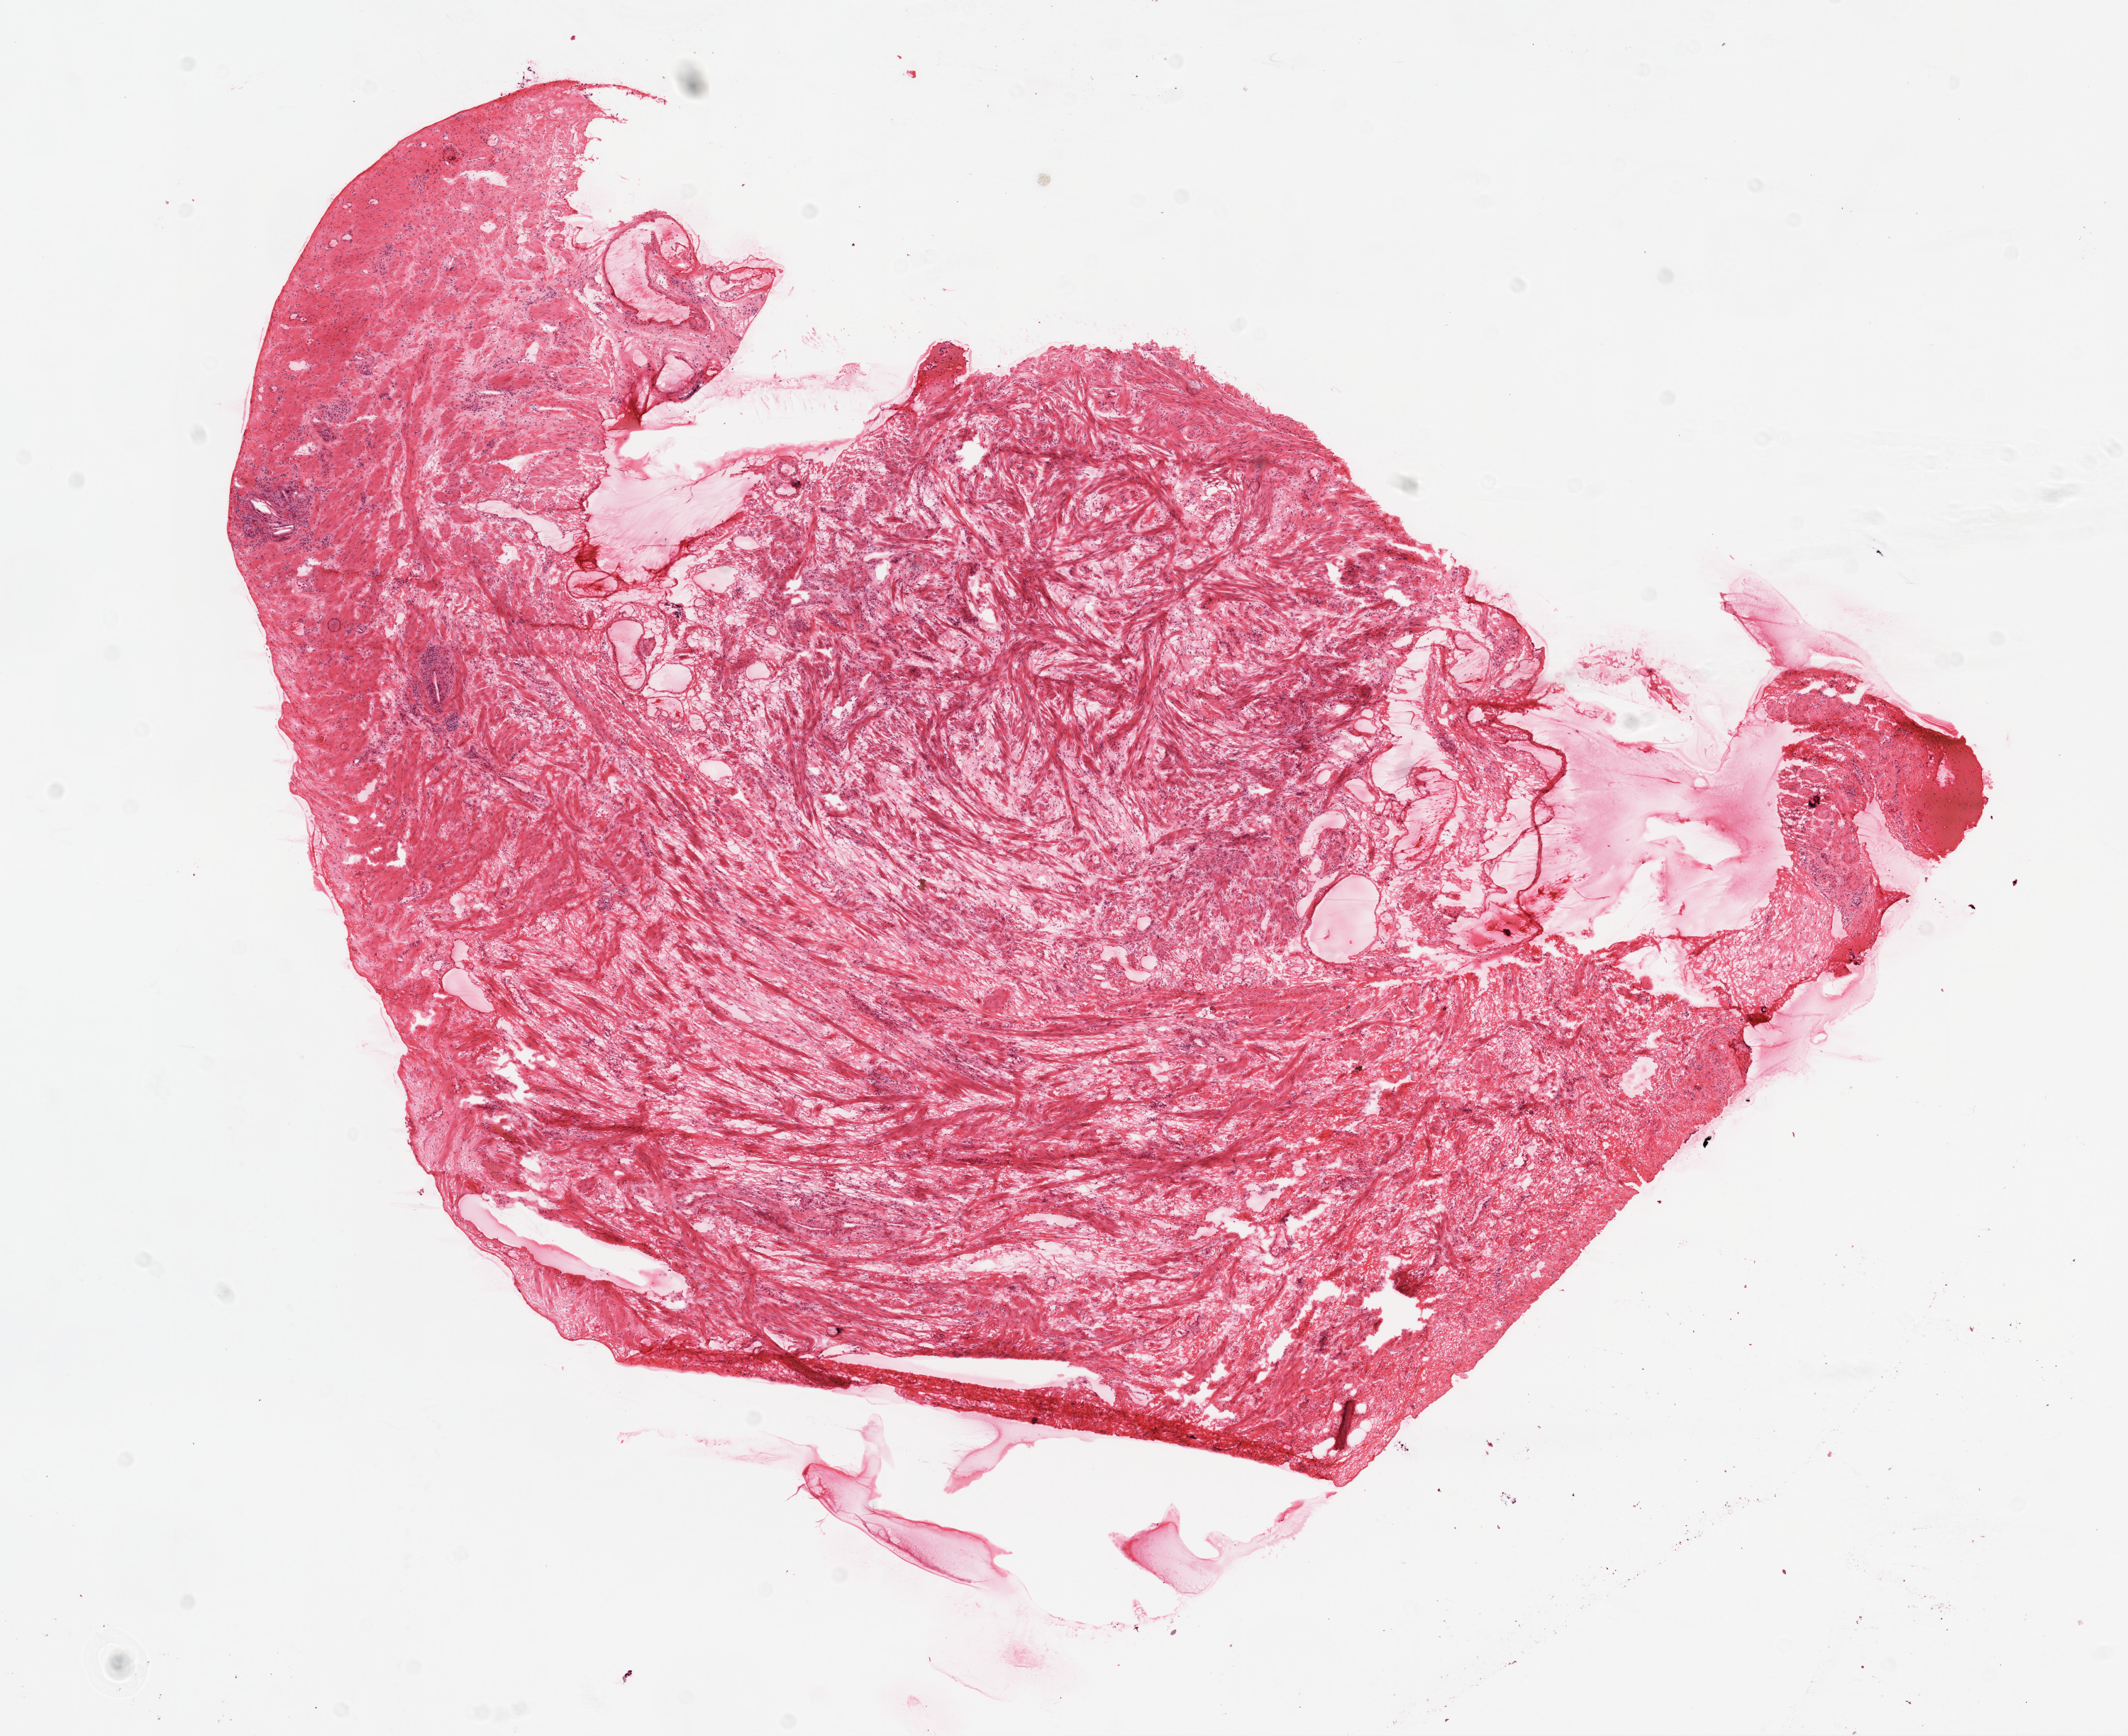
Digitized H&E-stained tissue section (whole slide) — whole scanned area (about 12.0 x 9.8 mm, slide scanned at 20x) shown as a low-resolution overview; frozen section from the top of the tissue portion; ovary, solid tissue normal (non-tumour tissue) sample. Female, age 81 years at initial diagnosis.
- this section: solid tissue normal (non-tumour) sample from the same patient
- patient diagnosis: Serous cystadenocarcinoma, NOS